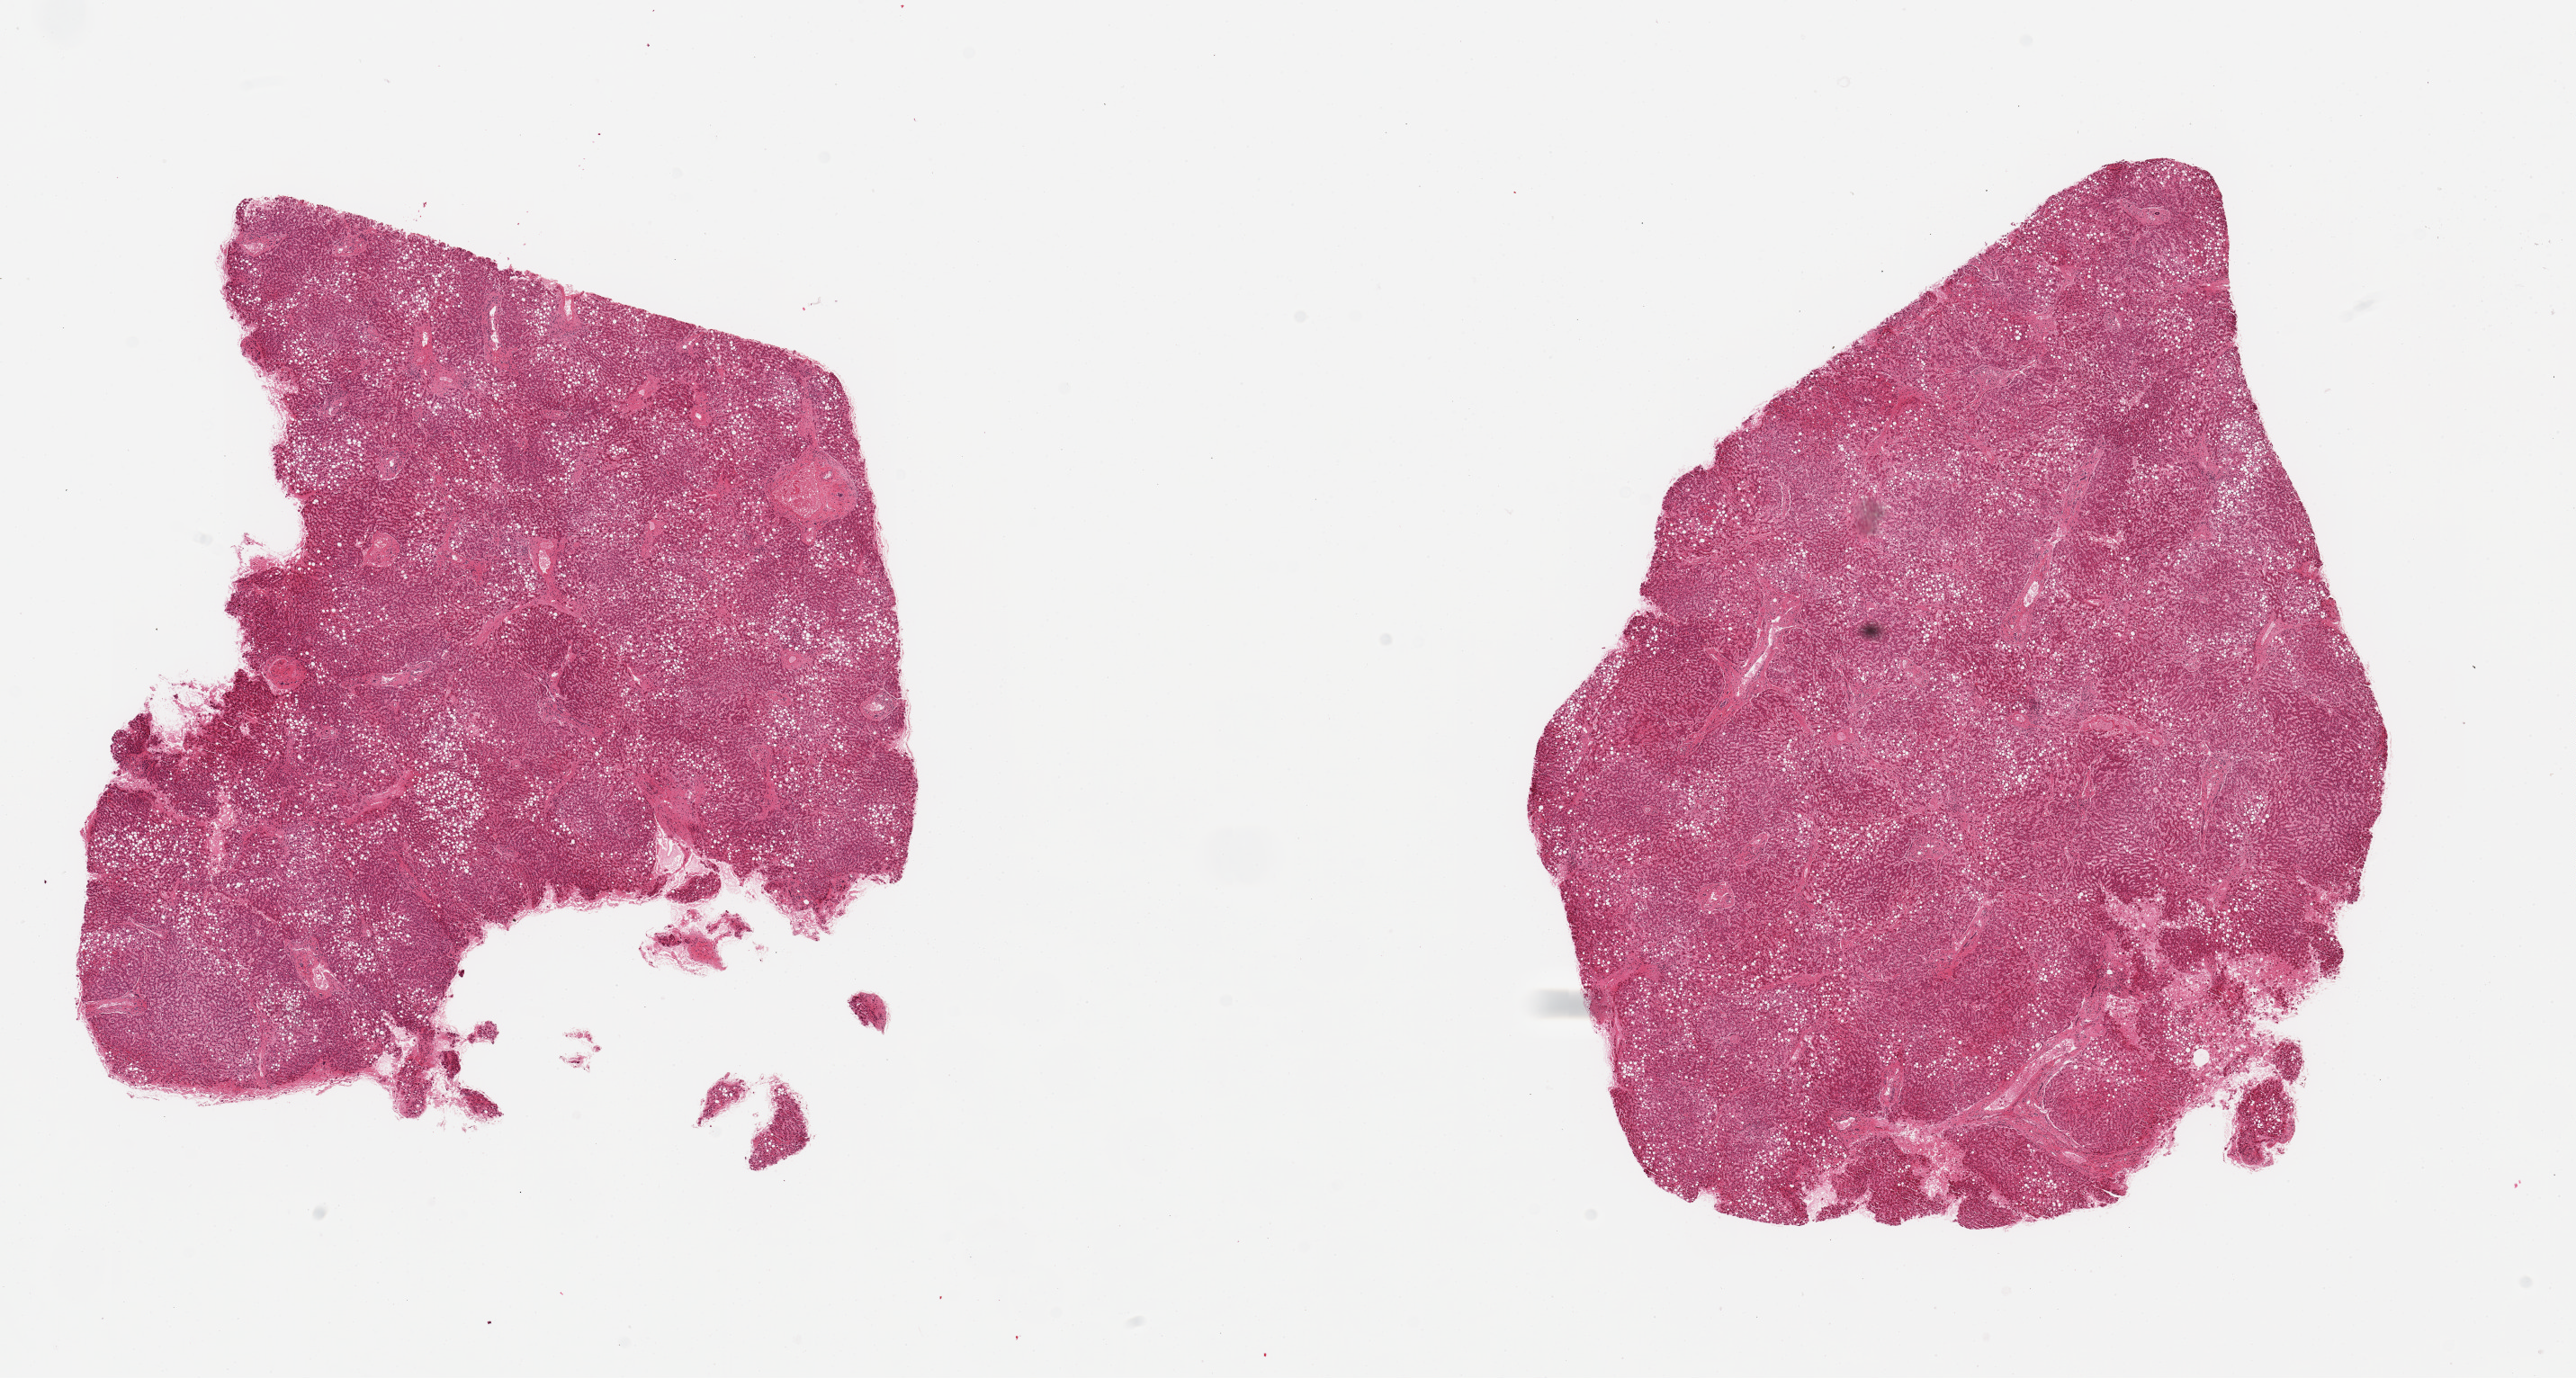
Digitized H&E-stained section — shown as a low-resolution overview of the whole scanned area (about 22.6 x 12.1 mm); PAXgene-fixed, paraffin-embedded tissue; target tissue: liver; tissue donor sample. Donor: female.
Review note (as recorded): 2 pieces, mild macrovesicular steatosis, mild congestion and fibrosis.